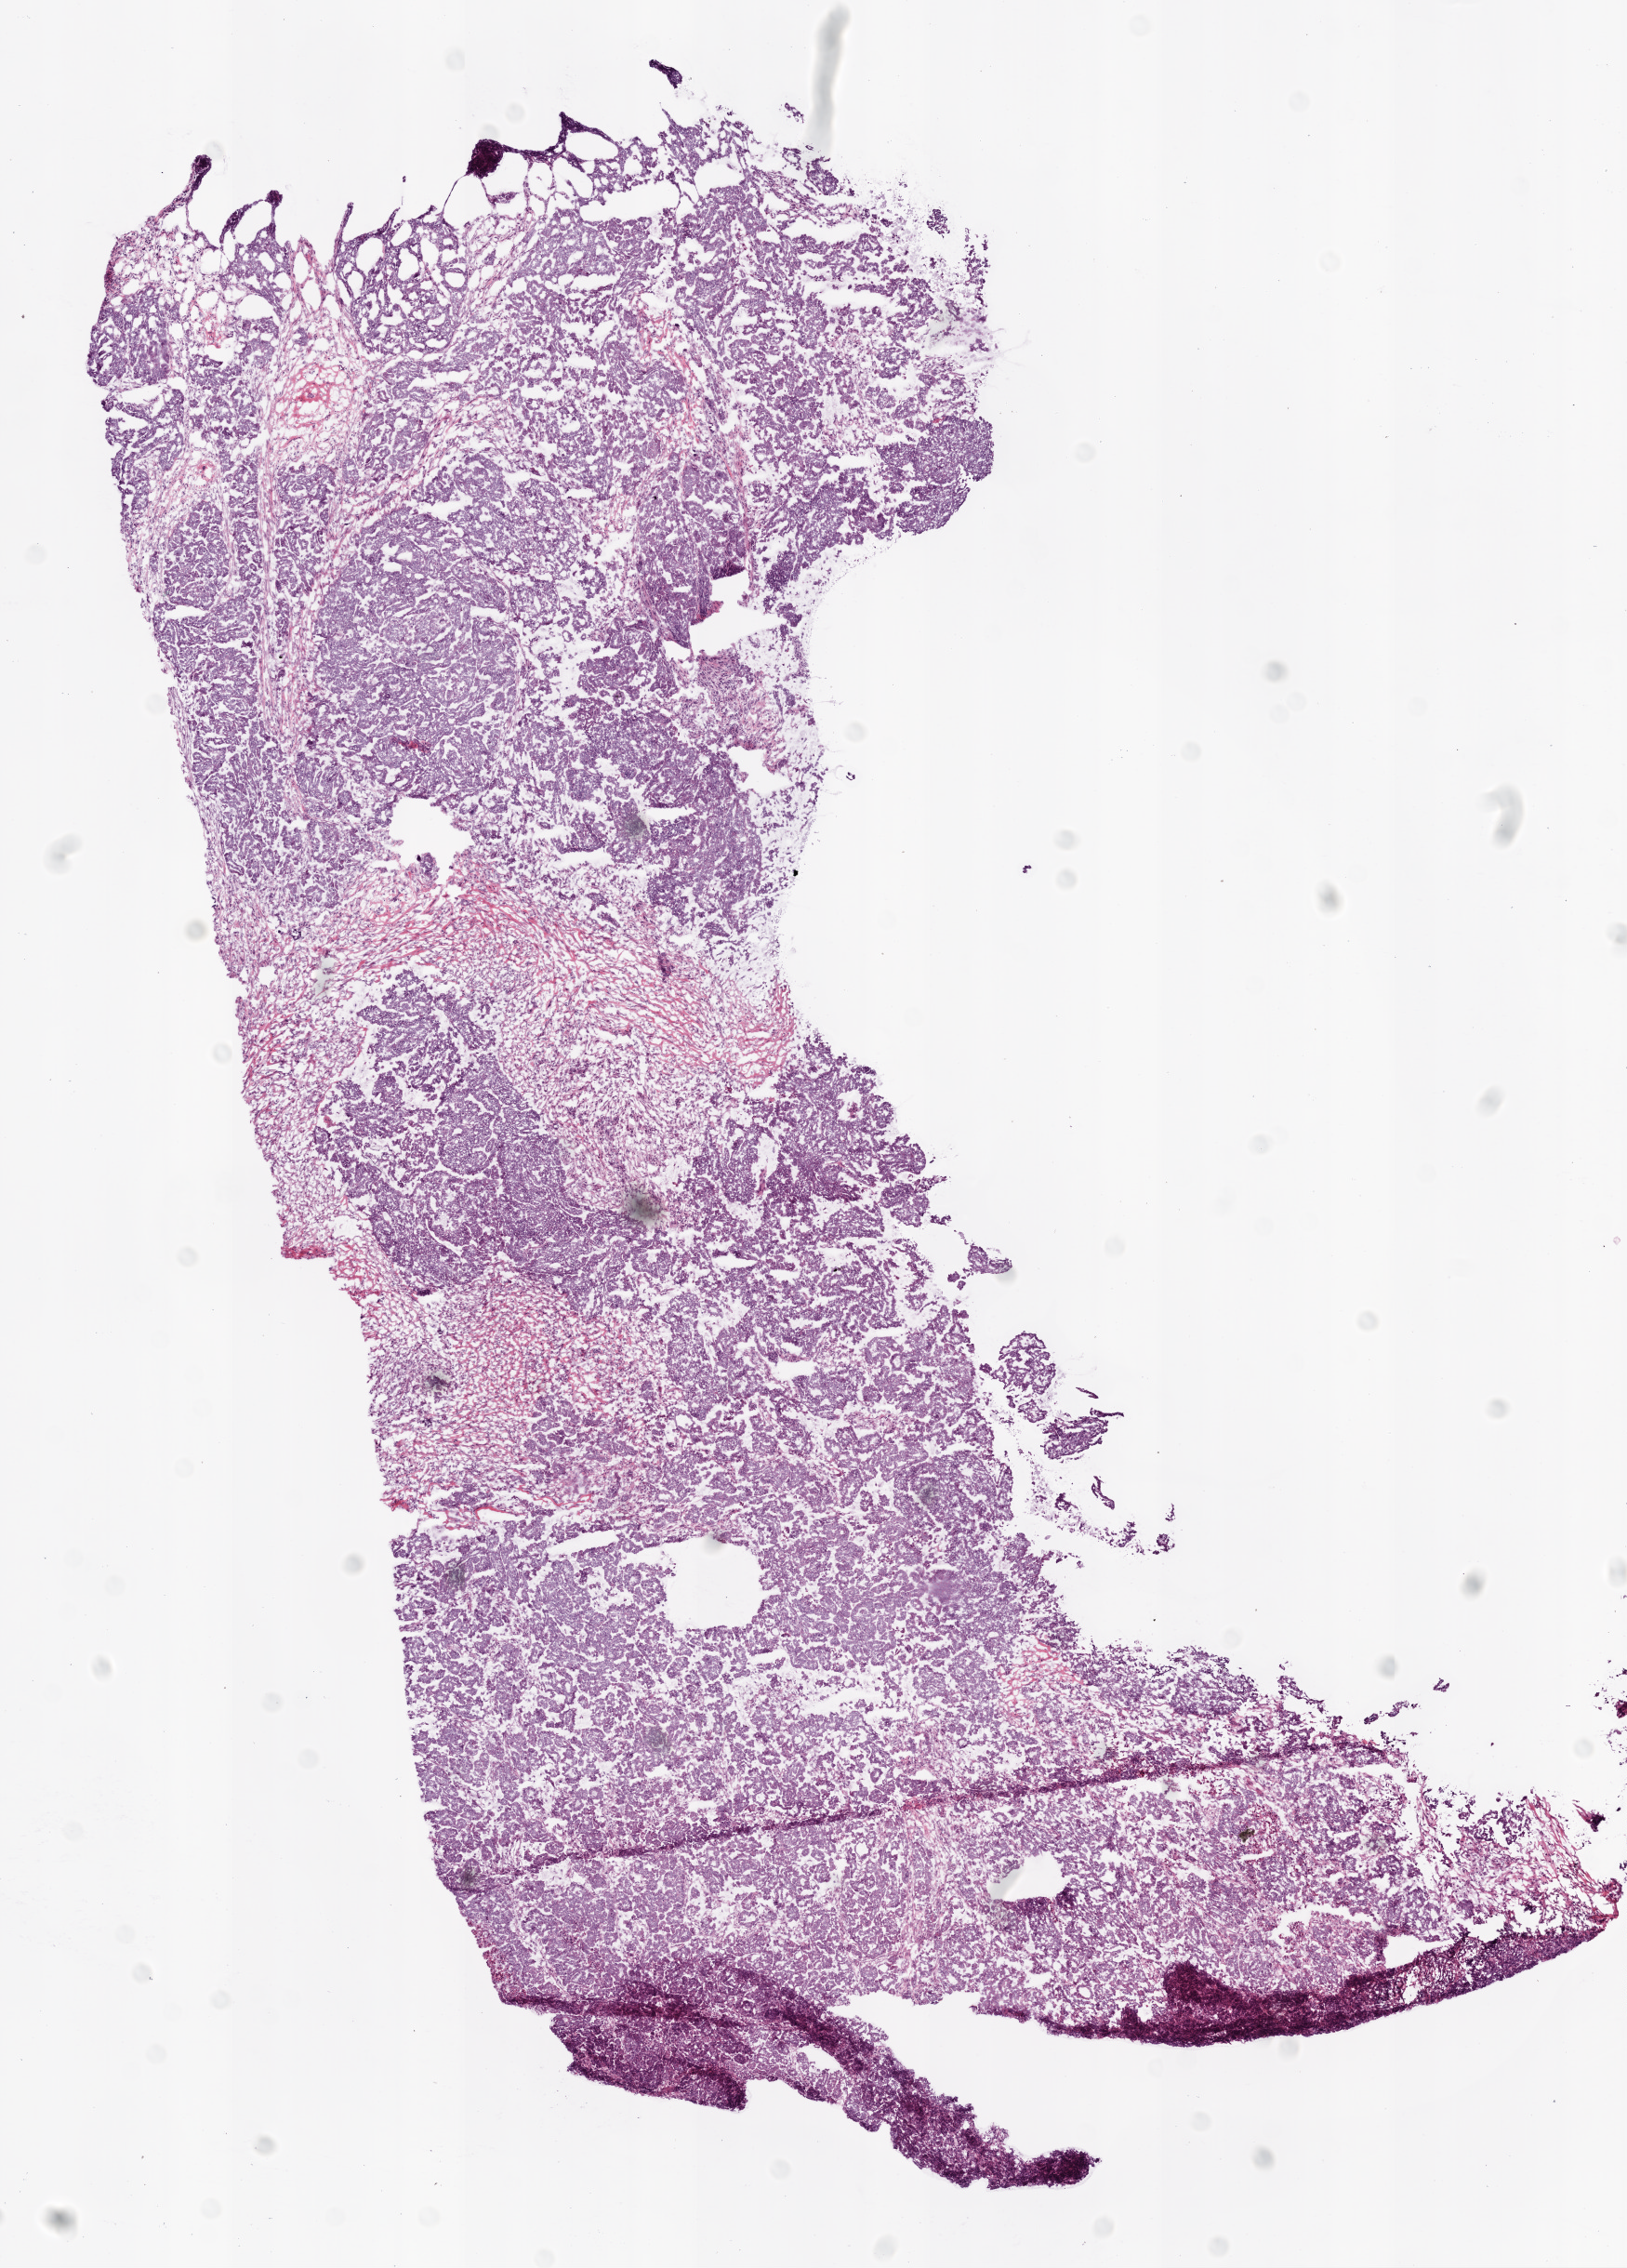
Hematoxylin and eosin (H&E) stained whole-slide image, low-resolution overview of the scanned area, about 7.0 x 9.8 mm (from a 20x scan). Frozen section. Sample: primary tumour, ovary. Female, age 40 years at initial diagnosis. Histologic grade: G3 (poorly differentiated). Slide review estimates, as recorded: tumour cells 90%, tumour nuclei 95%, normal cells 0%, stromal cells 0%, necrosis 10%.
- FIGO stage: IIIC
- laterality: bilateral
- diagnosis: Serous cystadenocarcinoma, NOS